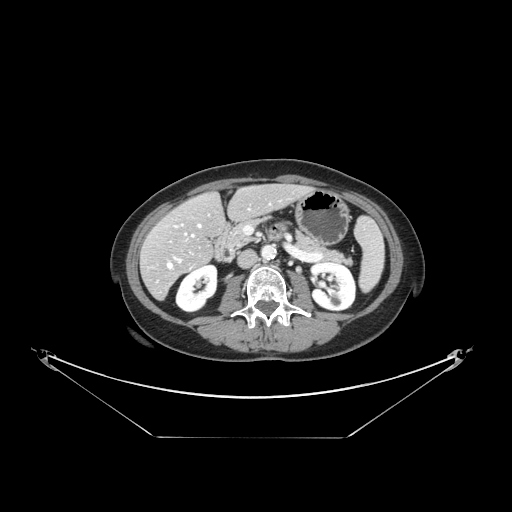
Contrast-enhanced abdominal CT, one axial slice; slice 58 of 148 in the series (ordered by position); reconstruction kernel STANDARD; 120 kVp; soft-tissue window (W 400 / L 40 HU); 2.5 mm slice thickness; 512 × 512 image matrix, field of view 500 × 500 mm. Female patient, age 73 years. From the clinical record (not read from this slice): diagnosis: colorectal cancer liver metastases, imaged before liver resection; multiple liver metastases: no; largest metastasis: 1 cm; disease in both lobes: no.
Outlined on this slice (outlined manually by an expert reader):
- hepatic veins: bounding box (x1, y1, x2, y2) in pixels: (167, 224, 201, 268)
- liver: (142, 185, 308, 298)
- planned liver remnant (the part of the liver to remain after resection): (164, 185, 307, 249)
- portal vein (with intrahepatic branches): (178, 259, 181, 262)